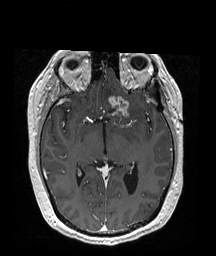
Brain MRI from a brain-tumour surgery series, one axial slice; T1-weighted post-contrast; 216 × 256 image matrix, field of view 211 × 250 mm. From the clinical record (not read from this slice): histopathology: Oligodendroglioma; WHO grade: 2; IDH mutation: yes; tumour location: Left Frontal (septal).
Annotated regions visible in this slice (outlined manually by an expert reader):
- tumour: box from (x=107, y=95) to (x=132, y=117) px